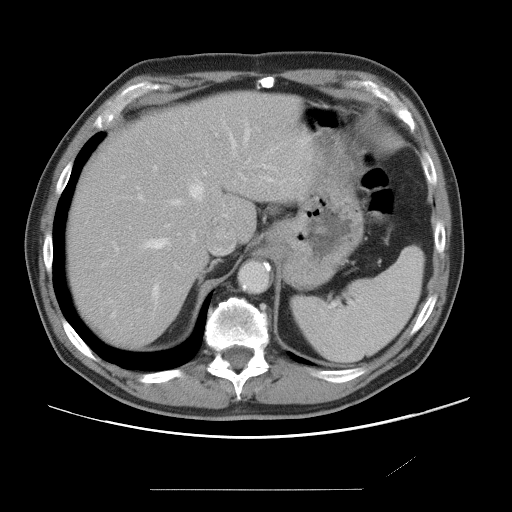
Contrast-enhanced abdominal CT, one axial slice. Position 56 of 87 along the scan axis. 120 kVp. Intravenous contrast given. Soft-tissue window (W 400 / L 40 HU). 512 × 512 image matrix, field of view 406 × 406 mm. Male patient, age 74 years. Case-level facts recorded for this patient, not image findings: diagnosis: colorectal cancer liver metastases, imaged before liver resection; multiple liver metastases: yes; largest metastasis: 1.1 cm; disease in both lobes: no.
Outlined on this slice (outlined manually by an expert reader):
- hepatic veins: box from (x=146, y=122) to (x=270, y=297) px
- liver: (x=68, y=93)–(x=307, y=349)
- planned liver remnant (the part of the liver to remain after resection): (x=68, y=93)–(x=306, y=349)
- portal vein (with intrahepatic branches): (x=113, y=166)–(x=207, y=251)